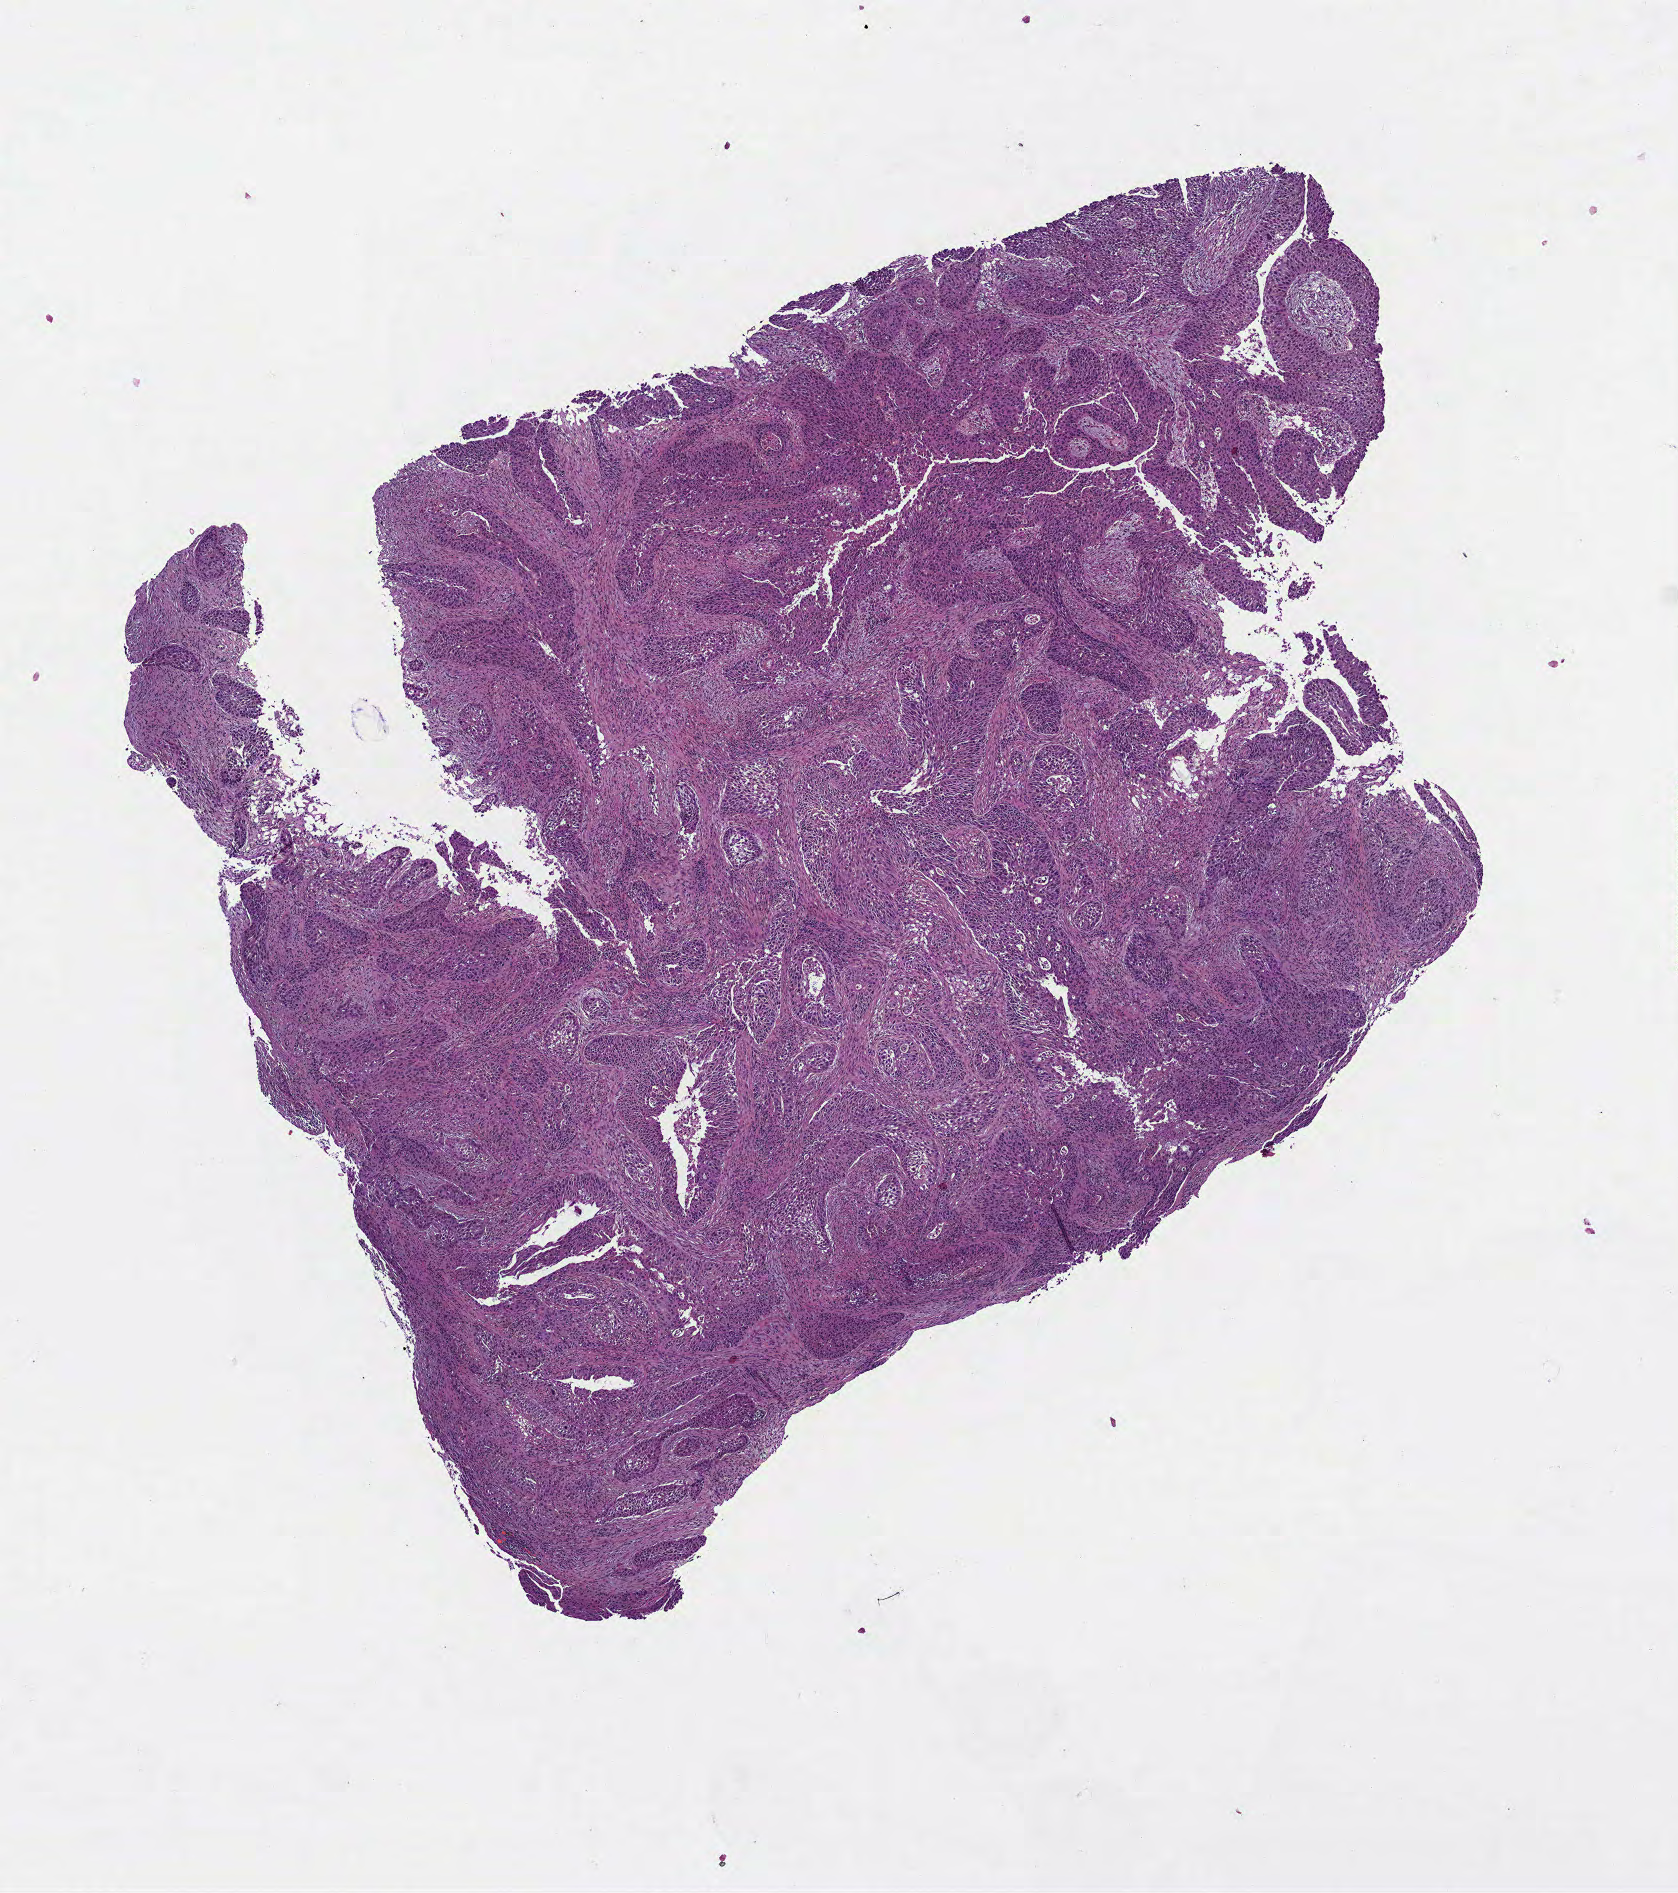
Whole-slide histology image, H&E — shown as a low-resolution overview of the whole scanned area (about 6.8 x 7.6 mm), formalin-fixed paraffin-embedded (FFPE) diagnostic section, primary tumour sample from the lung. Male, age 81 years at initial diagnosis.
- laterality: left
- AJCC pathologic stage: IA (7th edition)
- diagnosis: Squamous cell carcinoma, NOS (upper lobe, lung)